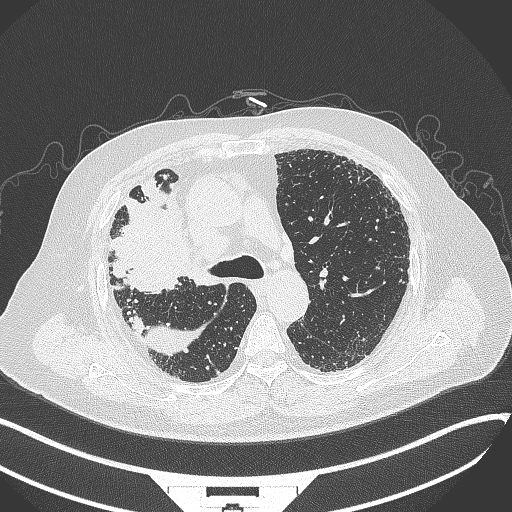
Chest CT, one axial slice. Slice 234 of 384 in the series (ordered by position). Reconstruction kernel B70f. 120 kVp. Lung window (W 1500 / L -600 HU). 512 × 512 image matrix. Patient: male, 69 years. Case-level facts recorded for this patient, not image findings: clinical TNM (as recorded): T4 N3 M1.
Outlined on this slice (bounding box drawn by a radiologist):
- lung tumour (recorded histology: adenocarcinoma): box from (x=103, y=186) to (x=189, y=301) px